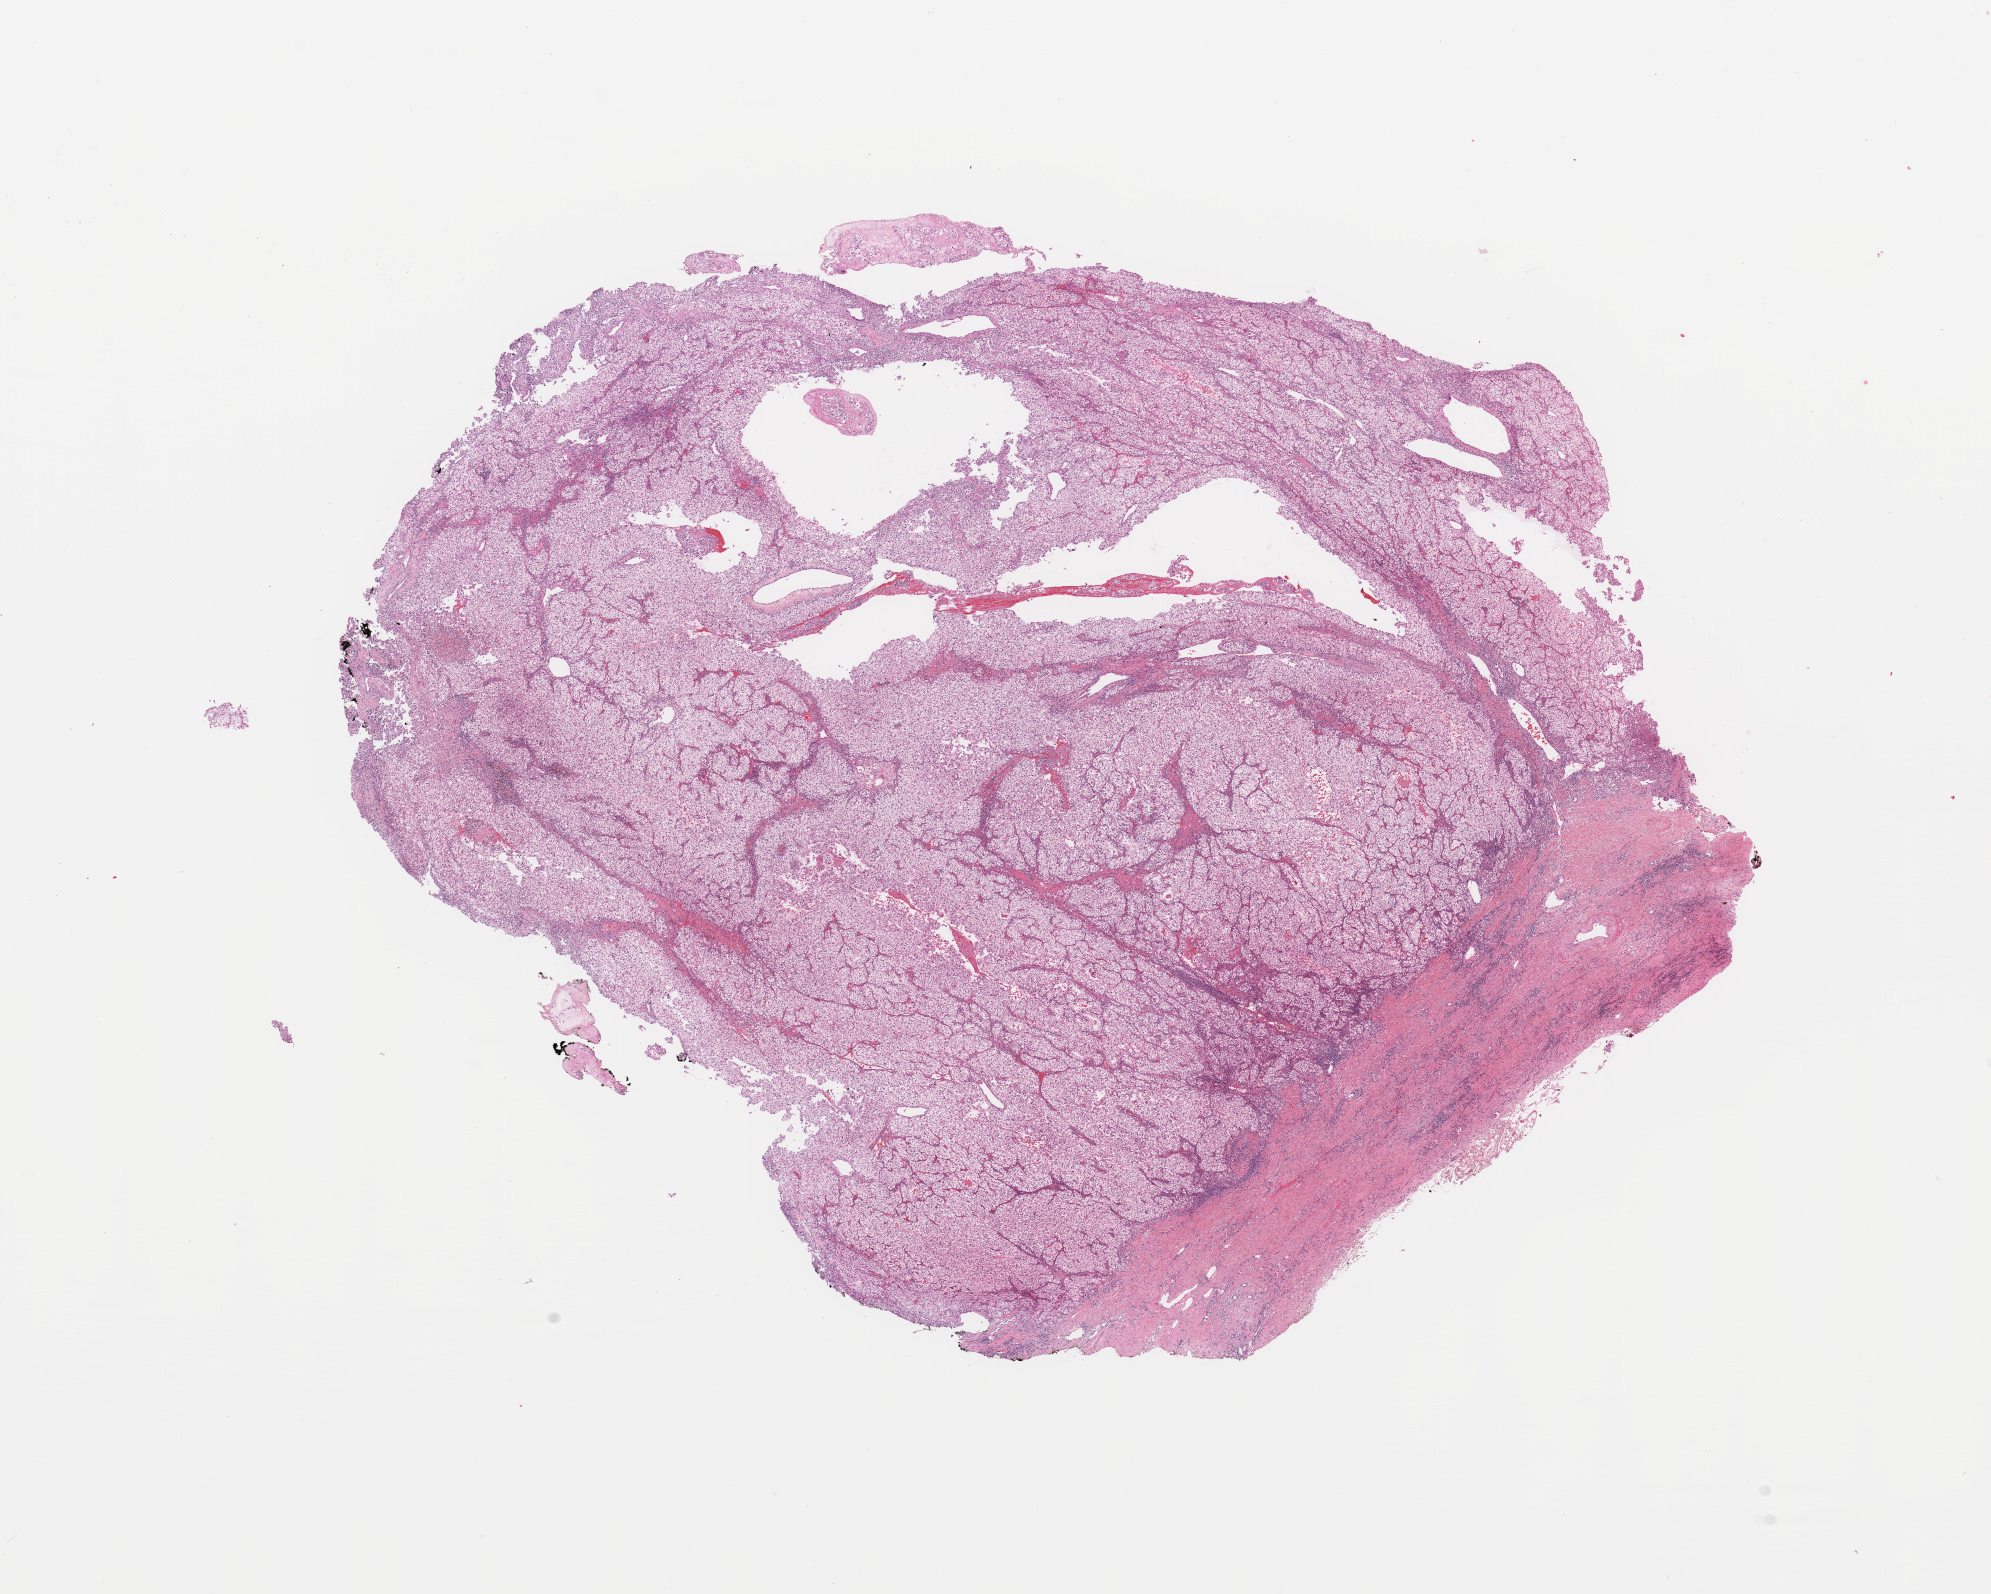
Digitized H&E-stained tissue section (whole slide), whole scanned area (about 15.8 x 12.6 mm, slide scanned at 20x) shown as a low-resolution overview; tumour tissue sample, sampled site: kidney. Patient: male, age 43 years. Histologic grade: G2 (moderately differentiated). Pathologist review of this section (percent, as recorded): tumour nuclei 85%, necrosis 0%.
Diagnosis: Renal cell carcinoma, NOS. AJCC pathologic stage: I.